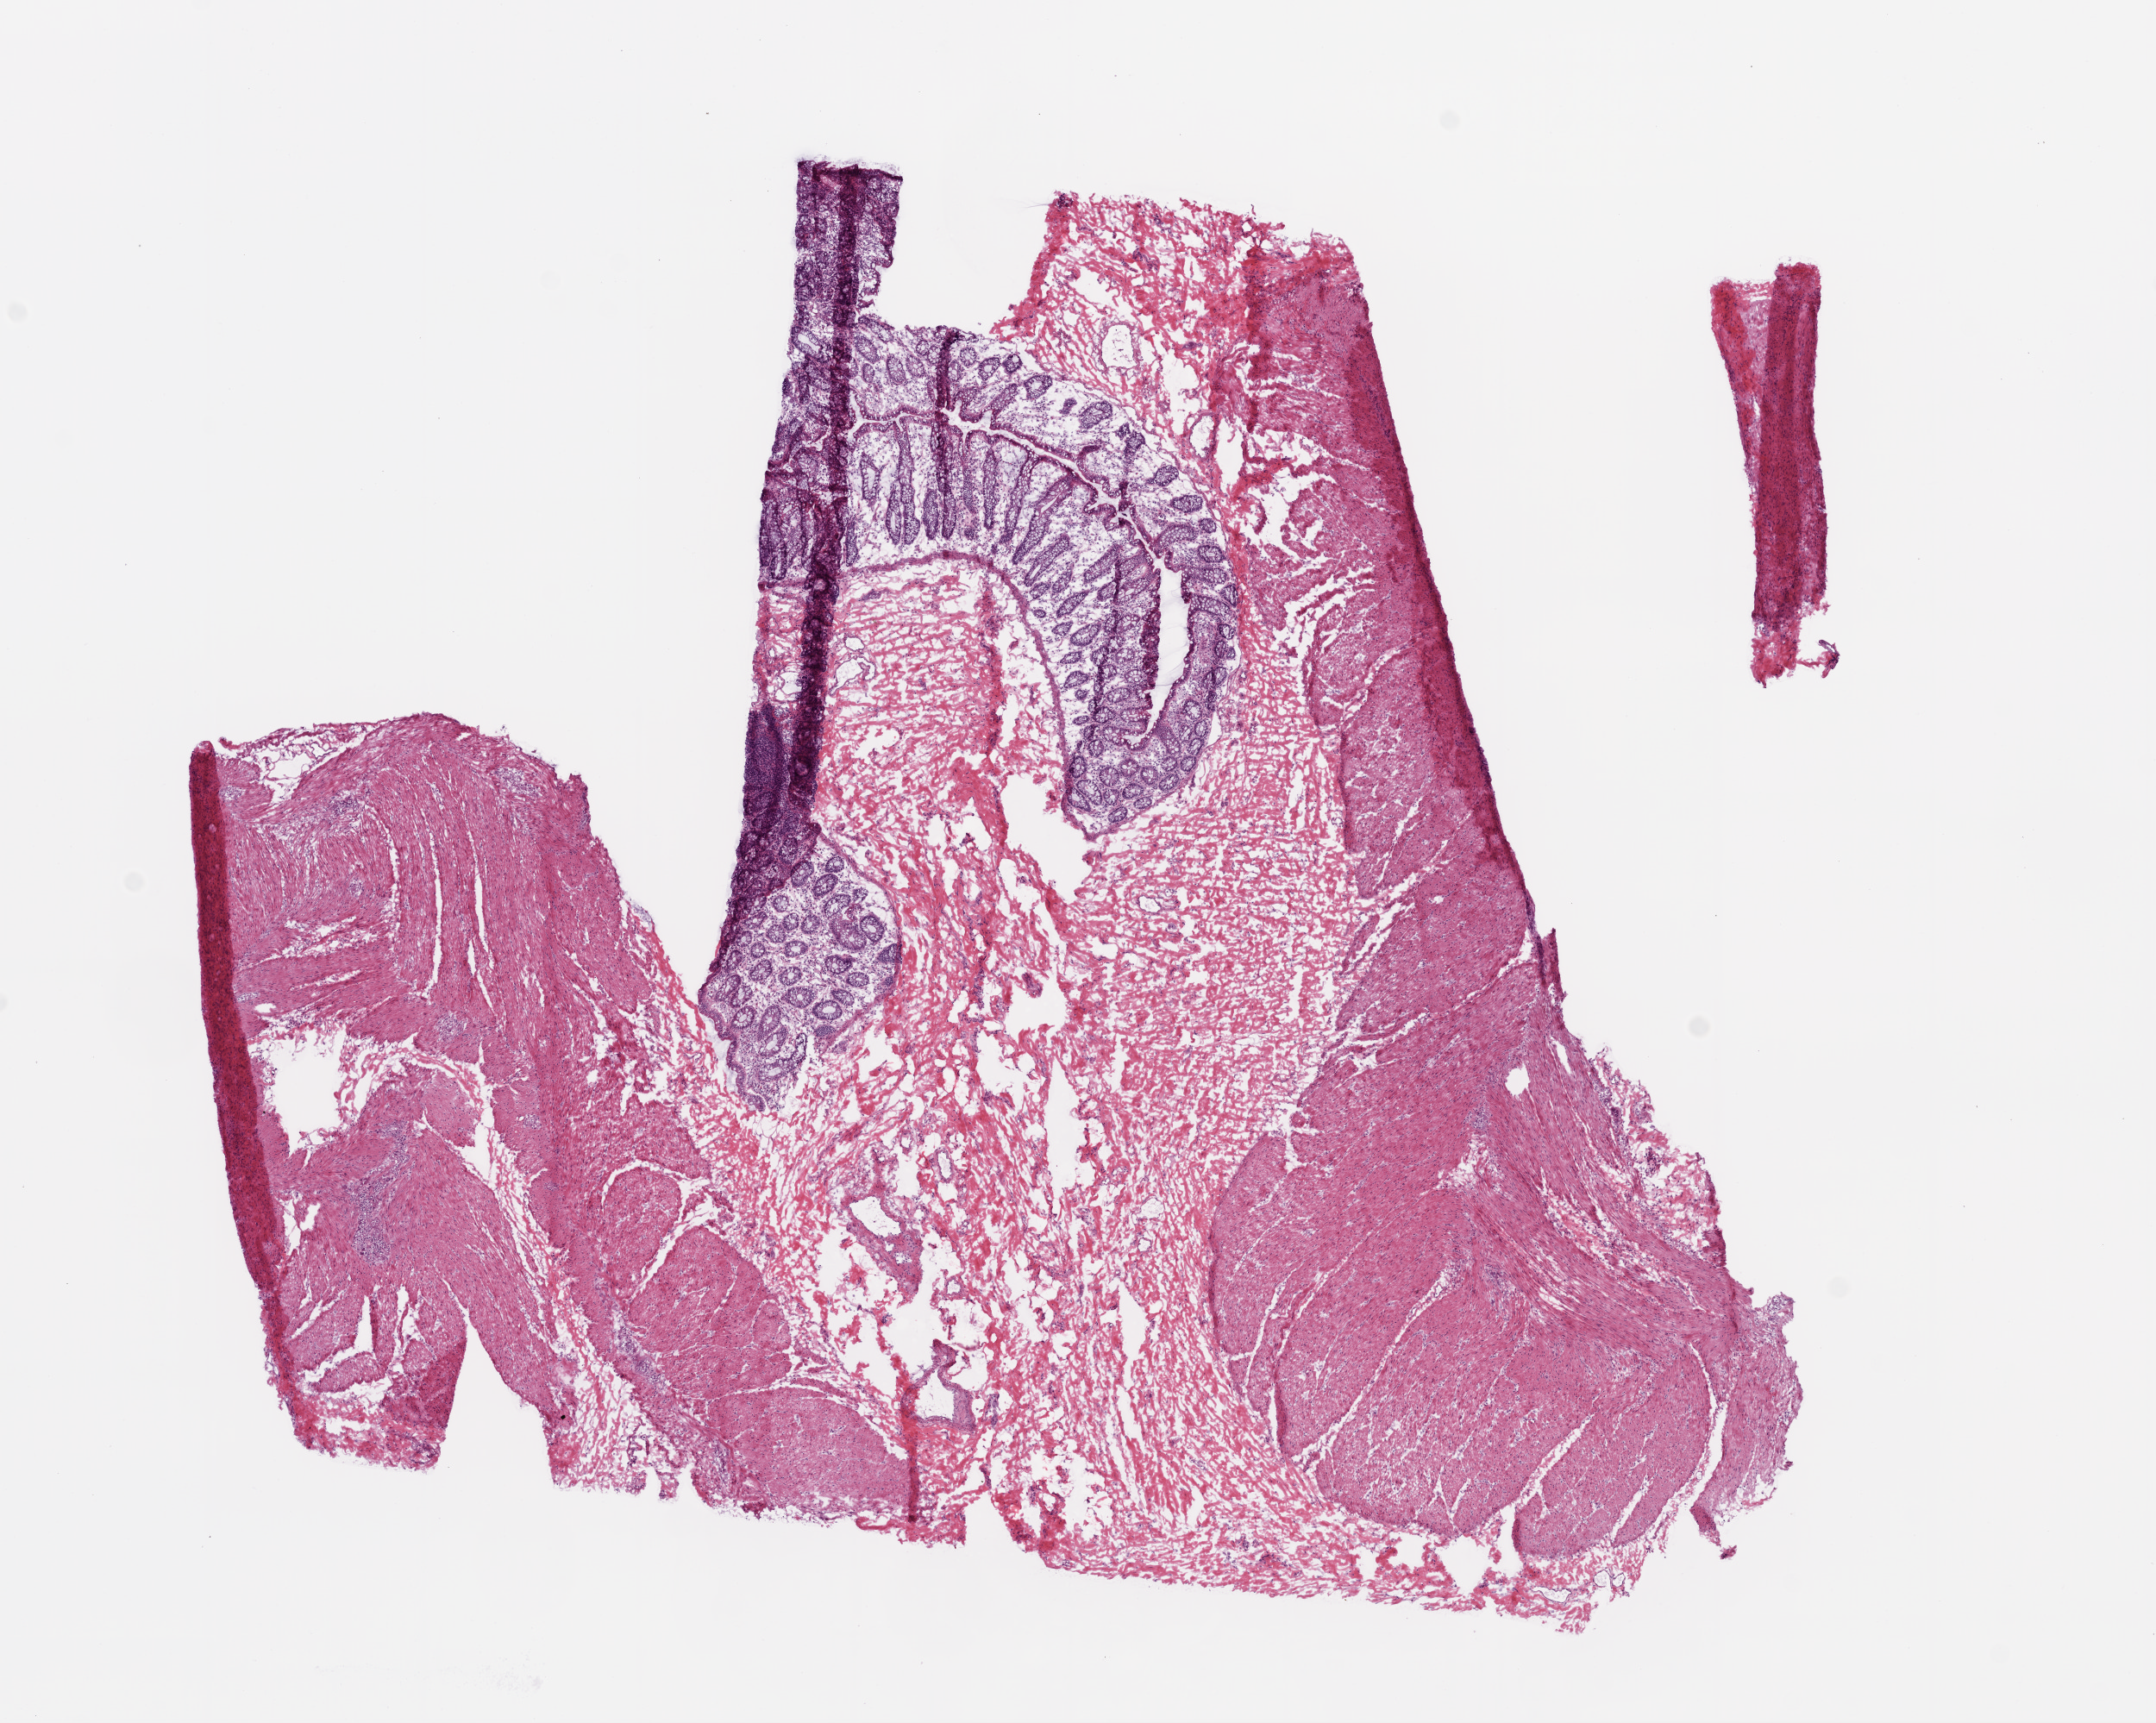
Digitized H&E tissue section (whole slide), whole scanned area (about 10.0 x 8.0 mm, acquisition: 20x scan) shown as a low-resolution overview; frozen section from the top of the tissue portion; solid tissue normal (non-tumour tissue) sample from the colon. Patient: male, age at initial diagnosis 77 years.
- this section: solid tissue normal (non-tumour) sample from the same patient
- patient diagnosis: Adenocarcinoma, NOS